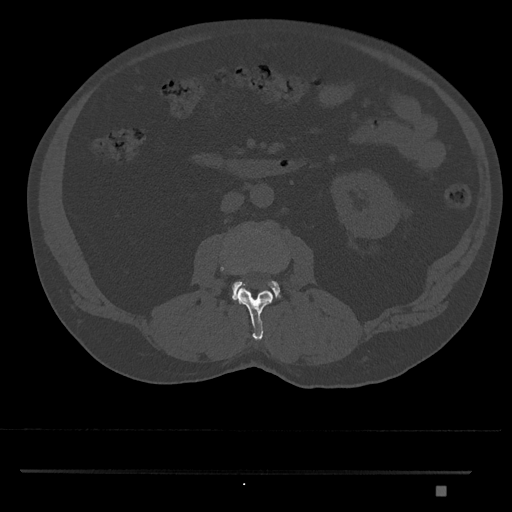
CT including the spine, one axial slice. Position 723 of 1134 along the scan axis. Reconstruction kernel Br40s/3. Bone window (W 1800 / L 400 HU). 0.5 mm slice thickness. 512 × 512 image matrix, field of view 429 × 429 mm. Male patient, age 65 years. From the clinical record (not read from this slice): primary cancer: prostate.
Structures marked on this image (semi-automatic segmentation, software-assisted and operator-edited):
- L2 vertebra: bounding box <221,265,273,341> (left, top, right, bottom; pixels)
- L3 vertebra: <232,280,281,303>